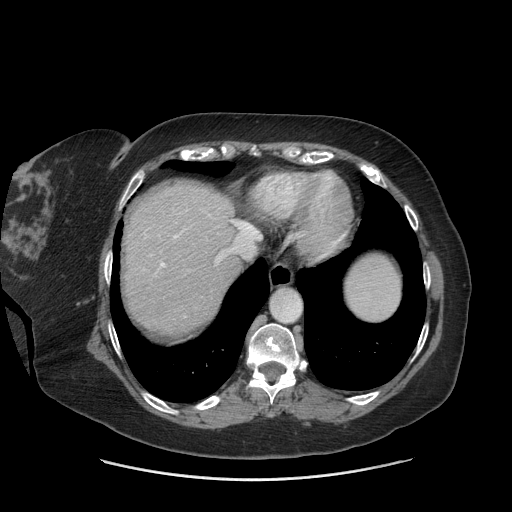
Contrast-enhanced abdominal CT (liver protocol), one axial slice. Slice 62 of 69 in the series (ordered by position). 140 kVp. Soft-tissue window (W 400 / L 40 HU). 2.5 mm slice thickness. 512 × 512 image matrix. Case-level facts recorded for this patient, not image findings: diagnosis: hepatocellular carcinoma (patient treated with transarterial chemoembolisation; whether this scan precedes or follows treatment is not stated here); TNM stage (as recorded): Stage-IIIB; Child-Pugh class: A; tumour differentiation: moderately differentiated; tumour nodularity: multinodular.
Structures marked on this image (semi-automatically segmented with operator editing):
- abdominal aorta: bounding box (x1, y1, x2, y2) in pixels: (271, 290, 300, 322)
- liver parenchyma outside the tumour (the mass and vessels are separate outlines, so this box may not span the whole liver): (122, 182, 242, 334)
- liver vessels: (160, 221, 235, 267)